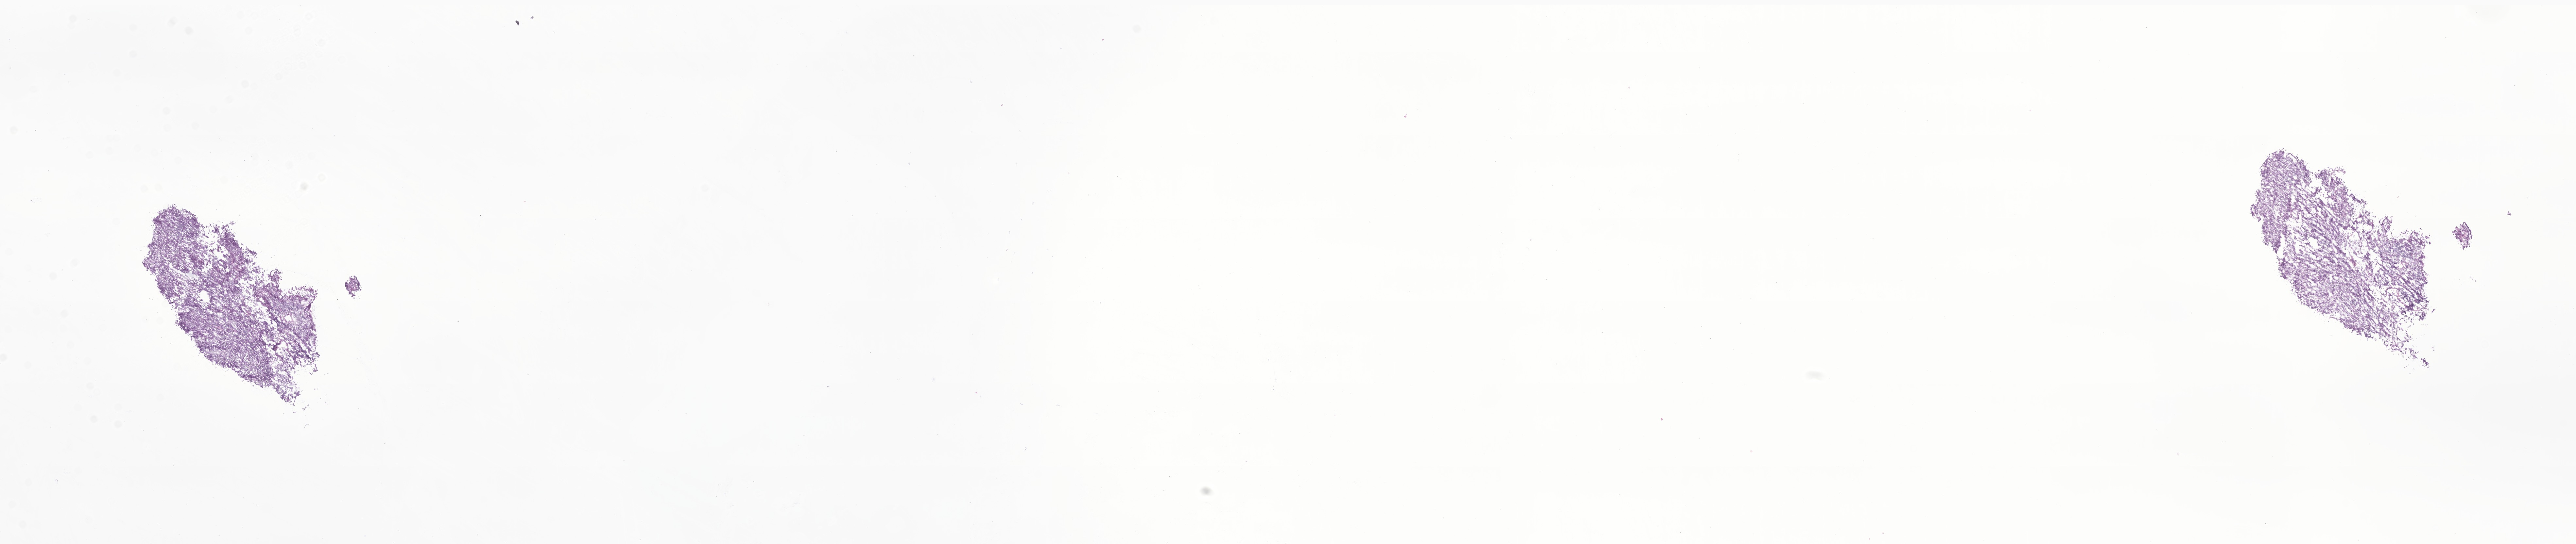
Digitized H&E-stained section of tumor tissue from the nasopharynx, a low-resolution overview of the entire scanned area, about 33.2 x 7.0 mm; frozen section. Patient: male, age 205 months (17 years 1 month).
- recorded diagnosis: Carcinoma, NOS